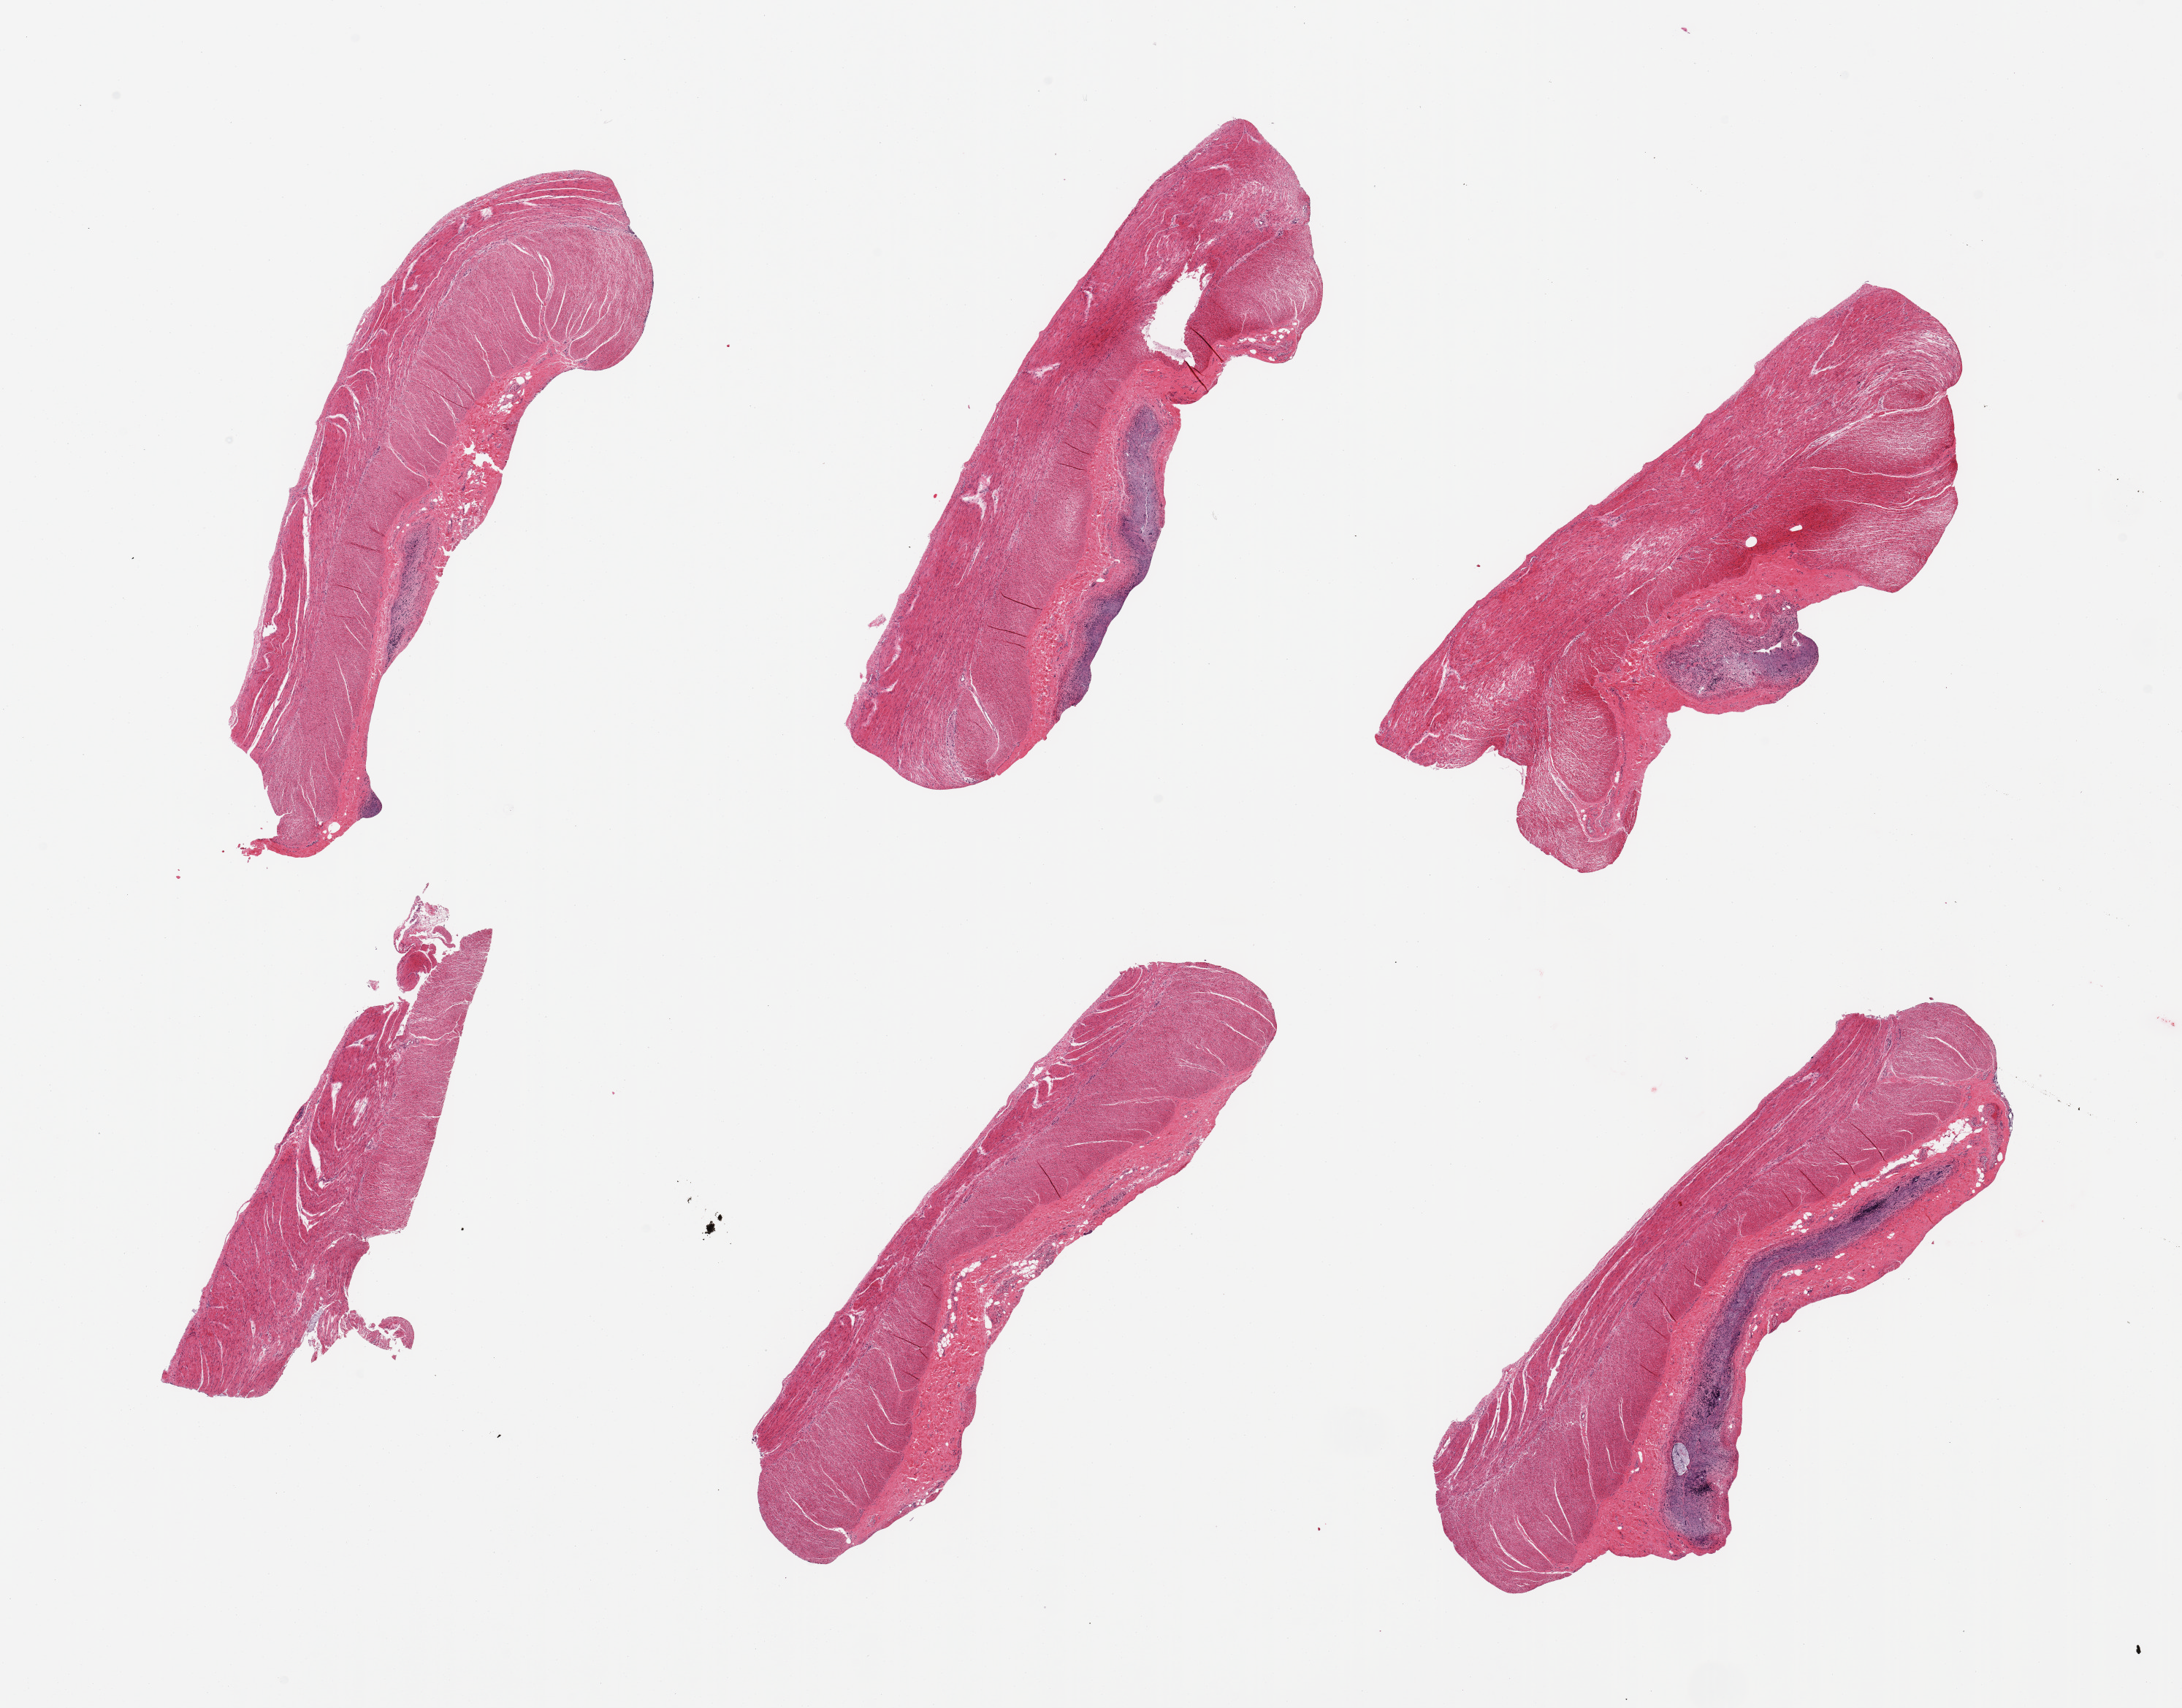
Digitized haematoxylin and eosin-stained section — whole scanned area (about 23.6 x 18.5 mm, from a 20x scan) shown as a low-resolution overview. PAXgene-fixed paraffin-embedded (PFPE) section. Target tissue: sigmoid colon. Tissue donor sample. Male donor.
- review note (as recorded): 6 pieces target muscularis, trace adherent but completely autolyzed mucosa 'contaminants' present